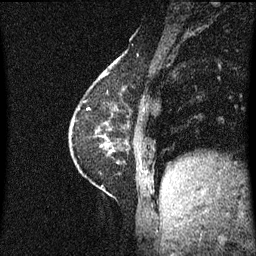
Breast MRI (dynamic contrast-enhanced), one sagittal slice; slice 16 of 60 in the series (ordered by position); dynamic contrast-enhanced series, image 2 of 3 at this slice position (ordered by acquisition); 1.5 T; TE 4.2 ms, TR 8.4 ms; 2 mm slice thickness; 256 × 256 image matrix. Female patient, age 60 years.
Annotated regions visible in this slice (semi-automatic segmentation, software-assisted and operator-edited):
- analysis volume of interest (the breast-tissue region the enhancement analysis was run in; not a lesion): bounding box [x1, y1, x2, y2] px = [69, 68, 130, 193]
- tumour enhancement mask (voxels above the 70 % enhancement threshold inside the analysis volume of interest): [71, 68, 128, 153]